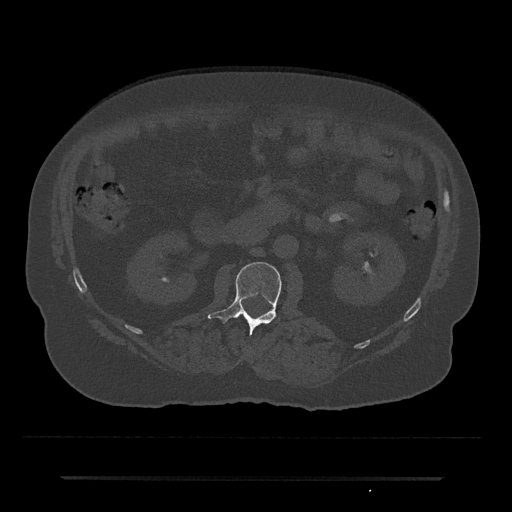
CT including the spine, one axial slice. Position 14 of 797 along the scan axis. Reconstruction kernel Br40s/3. Bone window (W 1800 / L 400 HU). 0.5 mm slice thickness. 512 × 512 image matrix, field of view 437 × 437 mm. Patient: male, 69 years. Case-level facts recorded for this patient, not image findings: primary cancer: prostate.
Structures marked on this image (semi-automatically segmented with operator editing):
- L2 vertebra: box from (x=208, y=262) to (x=282, y=335) px